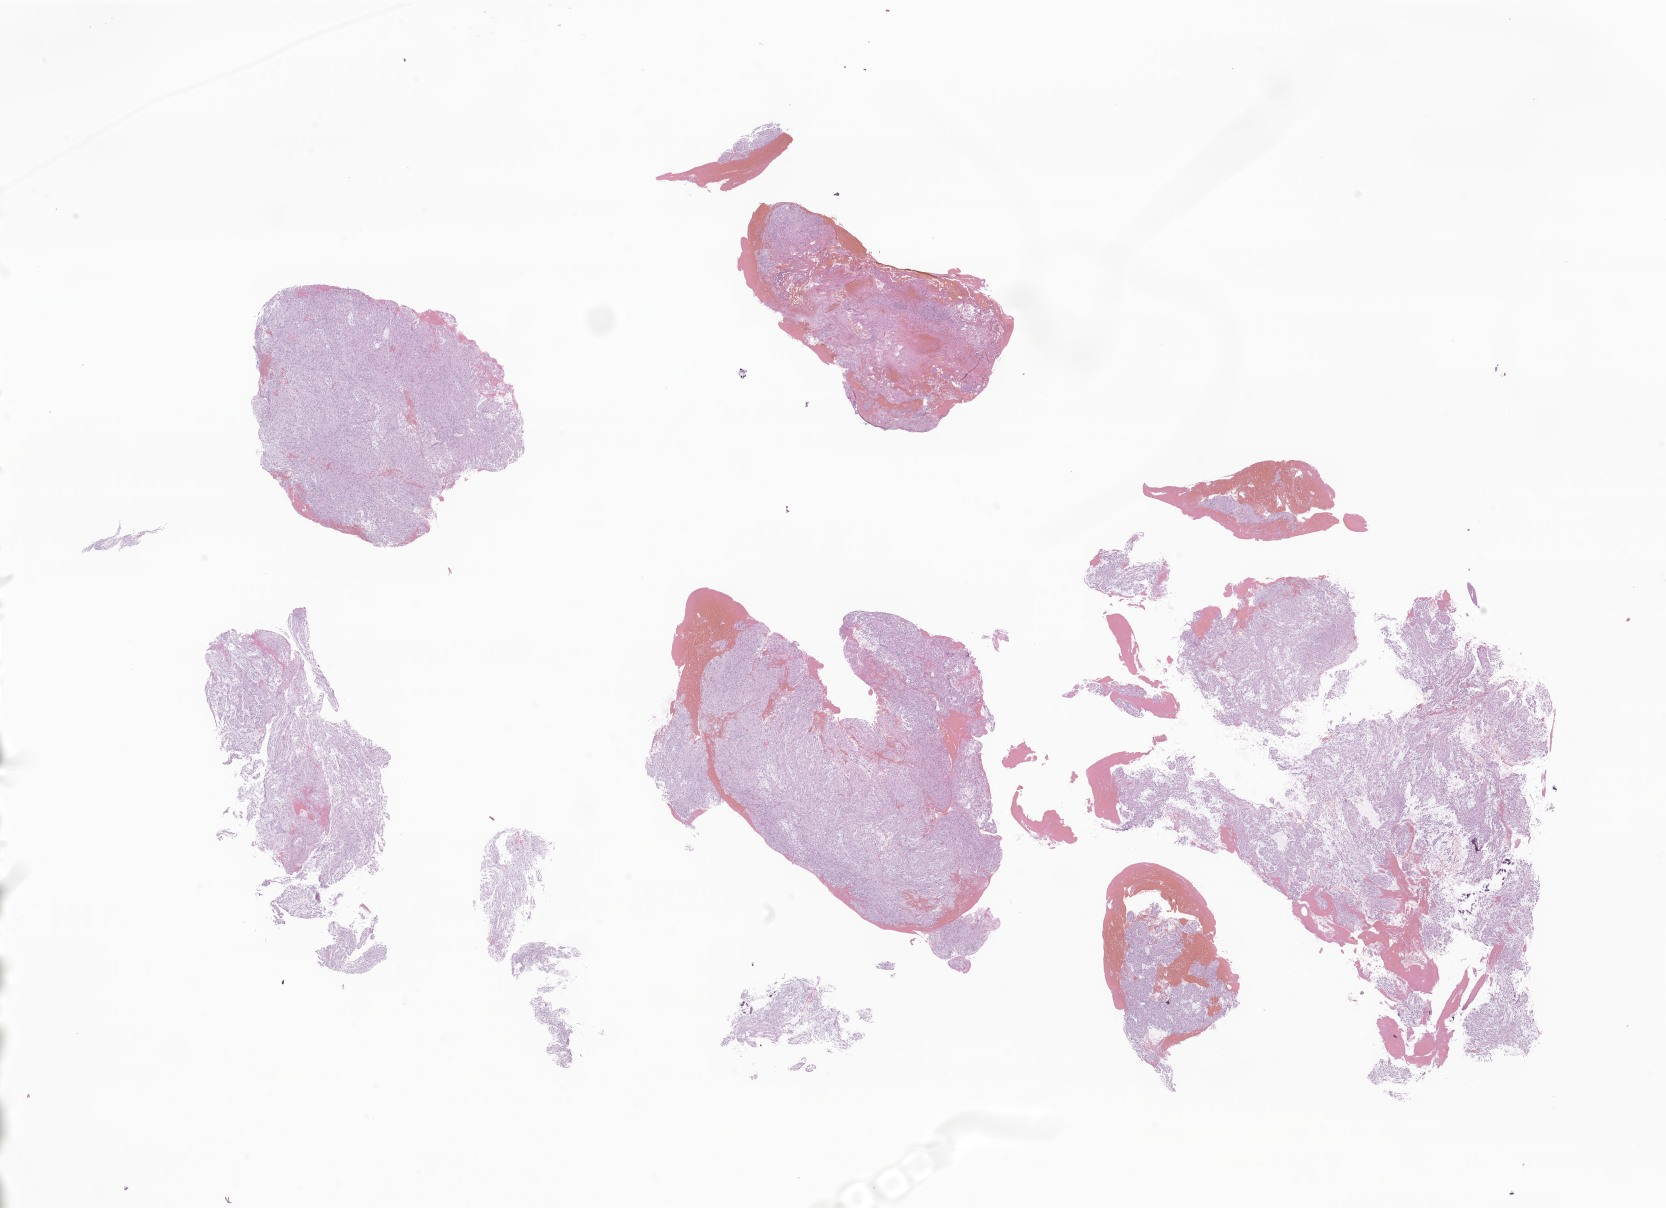
Digitized haematoxylin and eosin-stained section of tumor tissue from the brain, low-resolution overview of the scanned area, about 28.1 x 20.4 mm; formalin-fixed paraffin-embedded section. Patient: female, age 68 months (5 years 8 months).
Diagnosis: Pilocytic astrocytoma.